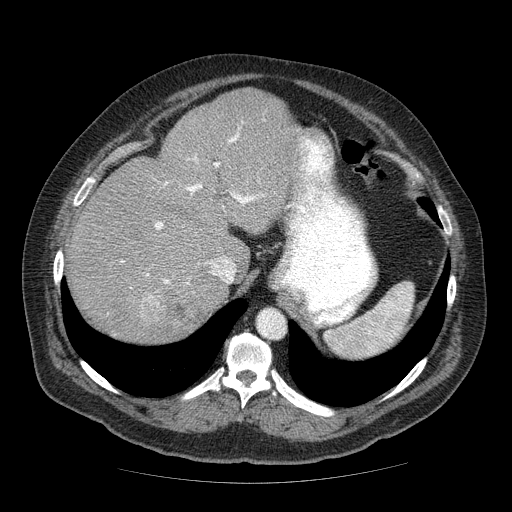
Contrast-enhanced abdominal CT (liver protocol), one axial slice; slice 48 of 85 in the series (ordered by position); reconstruction kernel STANDARD; soft-tissue window (W 400 / L 40 HU); 512 × 512 image matrix, field of view 420 × 420 mm. Case-level facts recorded for this patient, not image findings: diagnosis: hepatocellular carcinoma (patient treated with transarterial chemoembolisation; whether this scan precedes or follows treatment is not stated here); TNM stage (as recorded): Stage-IIIA; Child-Pugh class: A; tumour nodularity: multinodular; tumour size: 7 cm.
Annotated regions visible in this slice (semi-automatically segmented with operator editing):
- abdominal aorta: box from (x=257, y=309) to (x=285, y=339) px
- liver parenchyma outside the tumour (the mass and vessels are separate outlines, so this box may not span the whole liver): (x=68, y=88)–(x=304, y=344)
- mass: (x=137, y=289)–(x=214, y=342)
- liver vessels: (x=121, y=133)–(x=264, y=284)